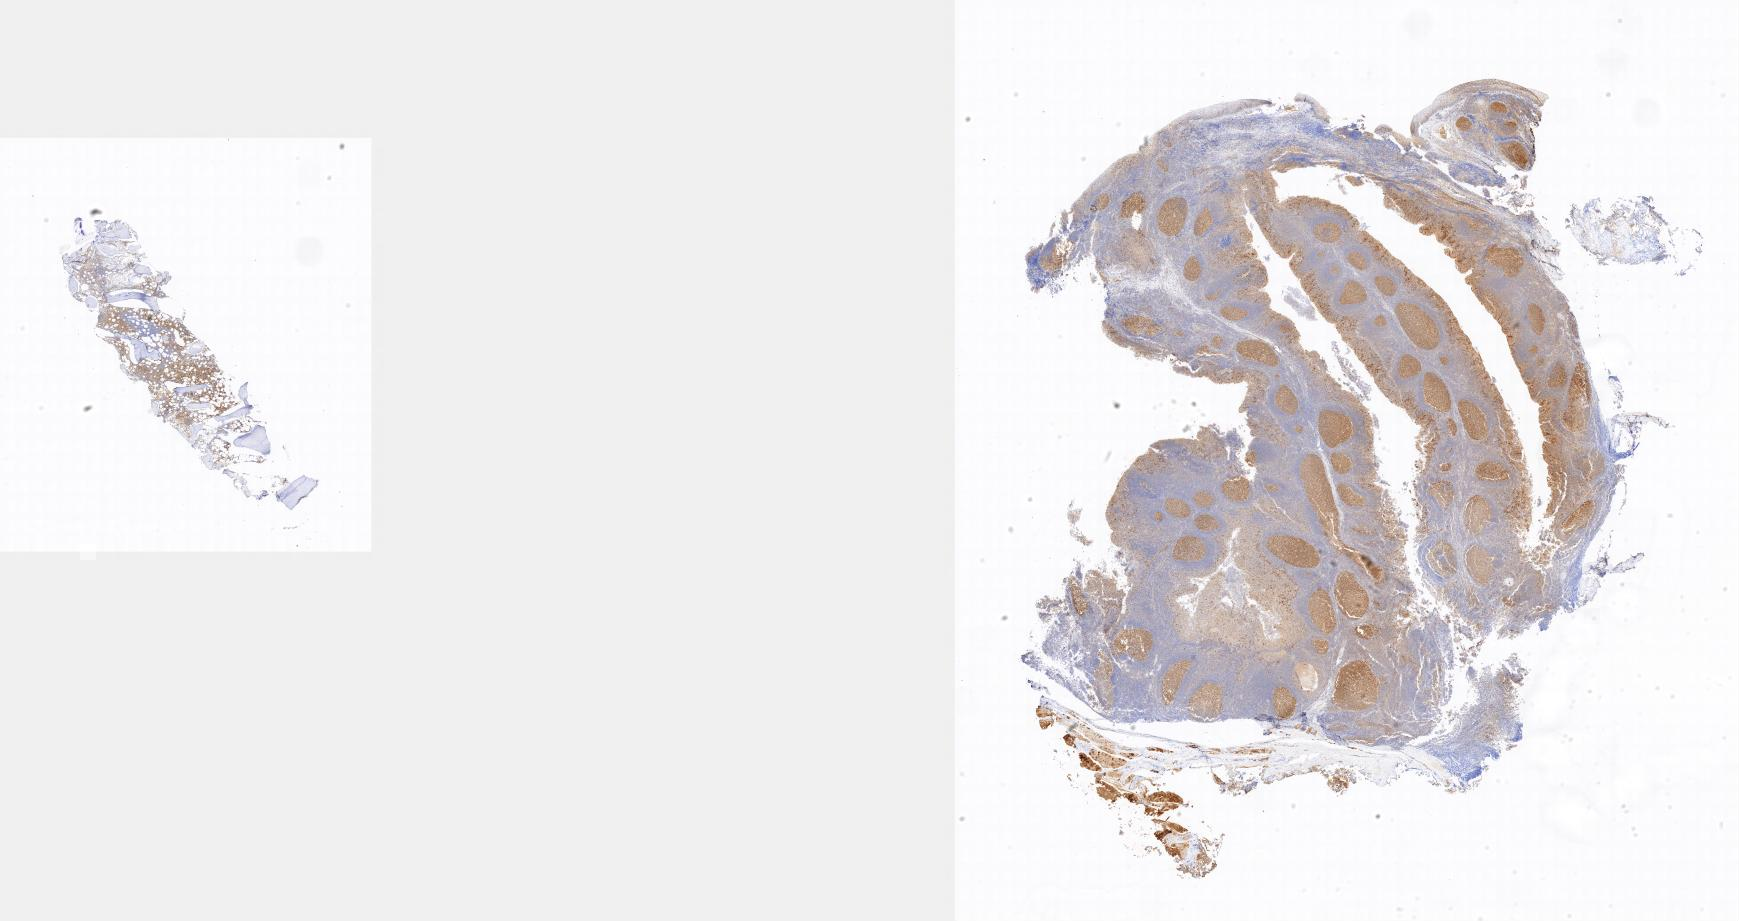
Immunohistochemistry (IHC) whole-slide image stained for BCL6 — whole scanned area shown as a low-resolution overview, specimen: tumor tissue, anatomic site: bone marrow. Patient: female, age at initial diagnosis 4 years.
- diagnosis: Burkitt lymphoma, NOS